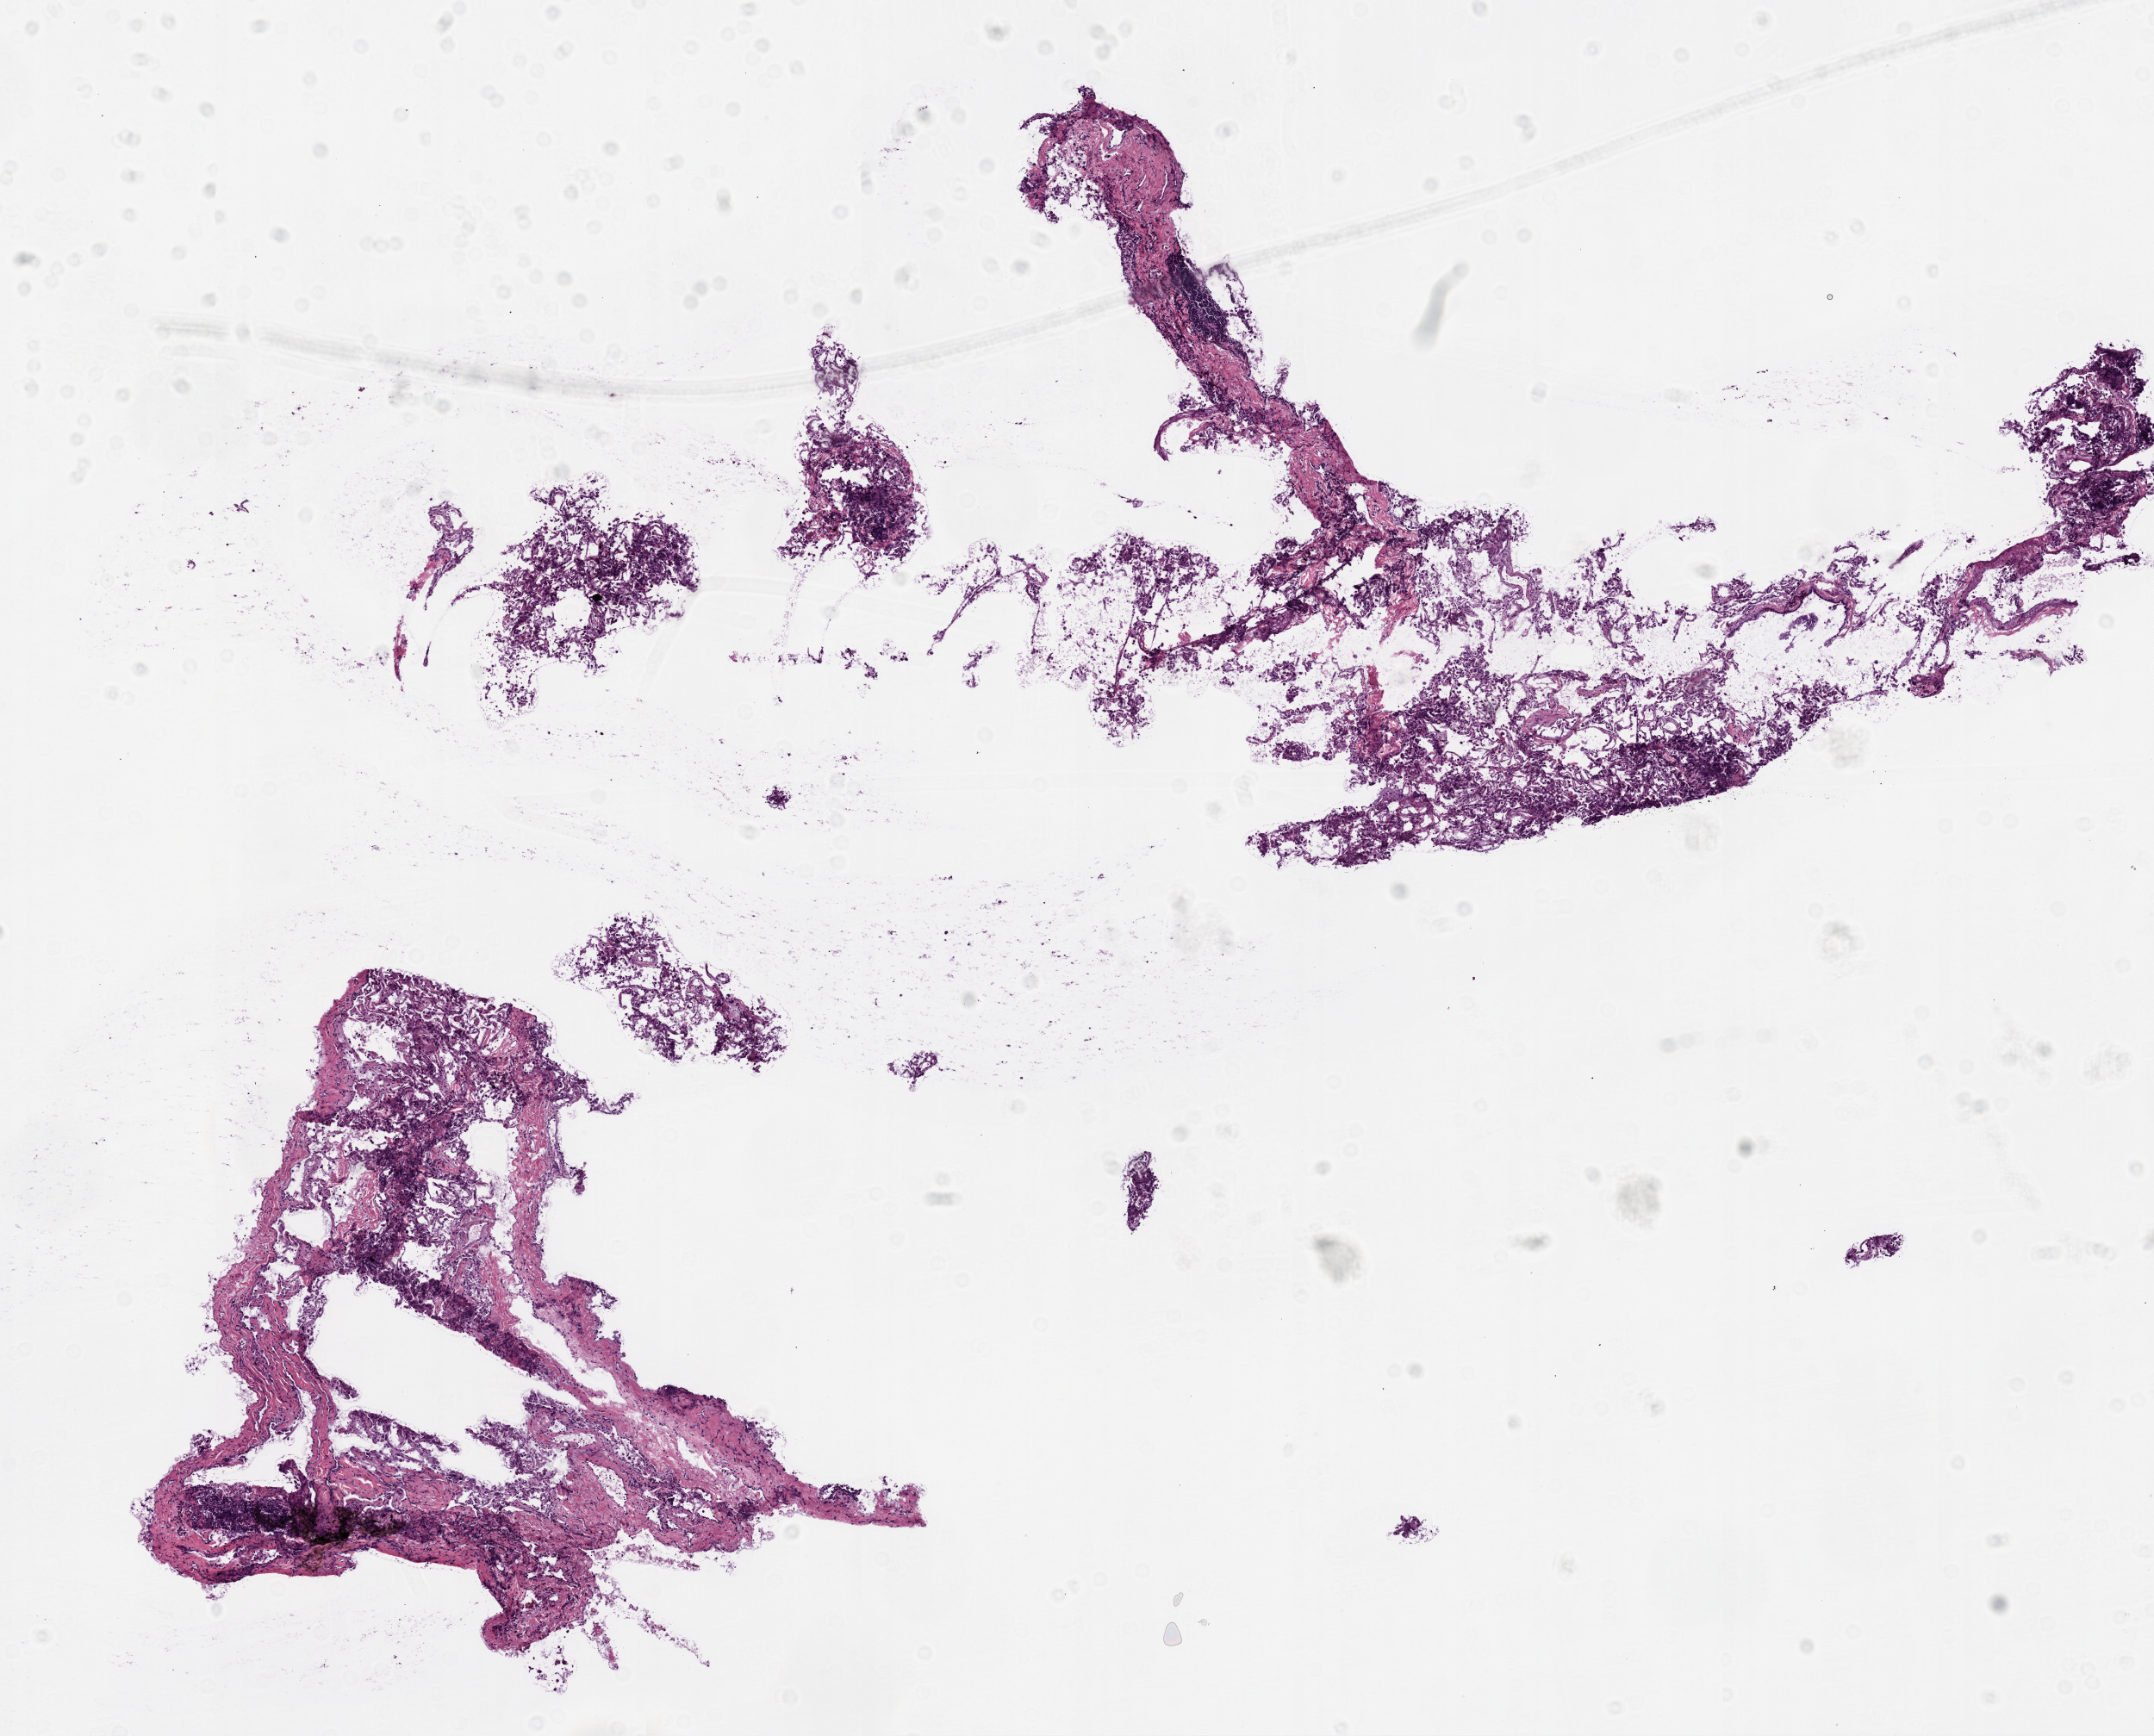
Hematoxylin and eosin (H&E) stained whole-slide image, whole scanned area (about 10.0 x 8.1 mm, from a 20x scan) shown as a low-resolution overview. Frozen section. Solid tissue normal (non-tumour tissue) sample from the lung. Male, age 73 years at initial diagnosis.
This section: solid tissue normal (non-tumour) sample from the same patient. Patient diagnosis: Squamous cell carcinoma, NOS (upper lobe, lung).